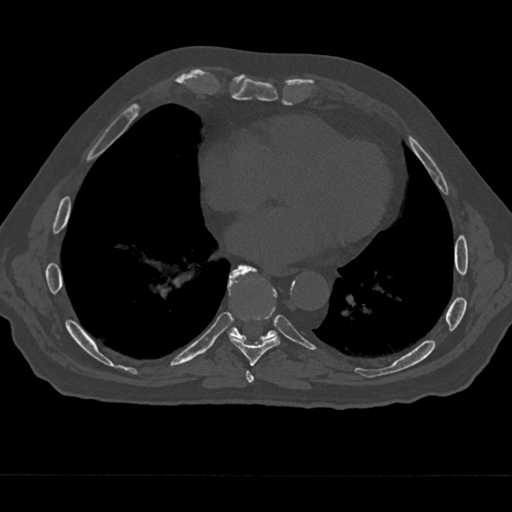
CT including the spine, one axial slice. Slice 297 of 797 in the series (ordered by position). Bone window (W 1800 / L 400 HU). 0.5 mm slice thickness. 512 × 512 image matrix, field of view 377 × 377 mm. Male patient, age 75 years. Case-level facts recorded for this patient, not image findings: primary cancer: renal.
Annotated regions visible in this slice (semi-automatic segmentation, software-assisted and operator-edited):
- T7 vertebra: bounding box <243,369,258,385> (left, top, right, bottom; pixels)
- T8 vertebra: <229,267,280,366>
- T9 vertebra: <227,264,277,342>